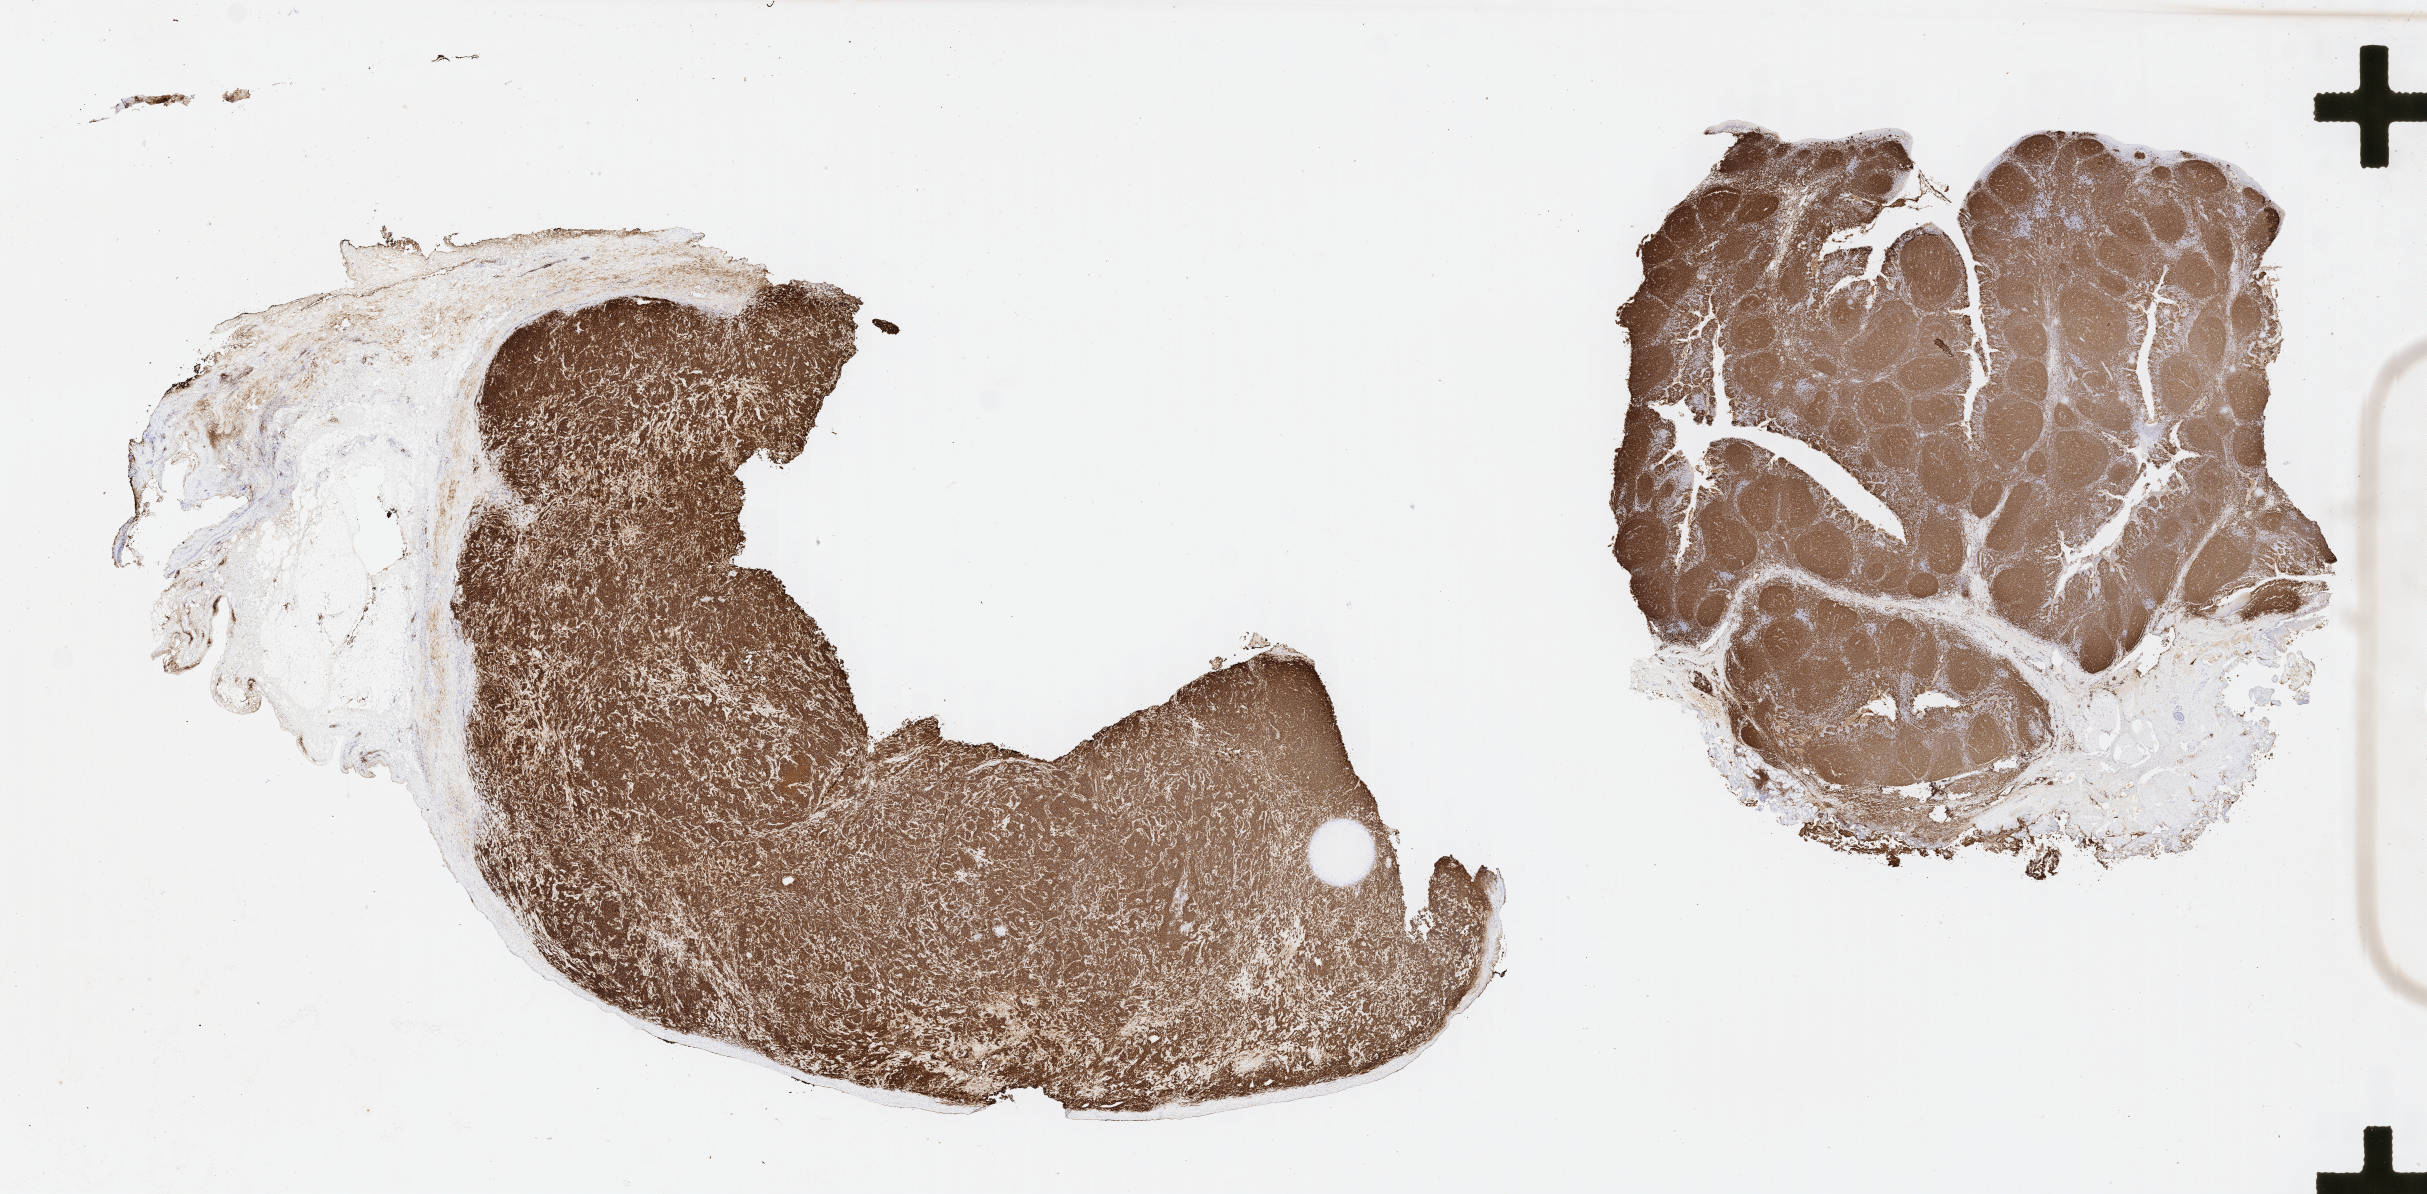
IHC for CD20, whole-slide image, shown as a low-resolution overview of the whole scanned area (about 39.2 x 19.3 mm). Tumor tissue. Anatomic site: bone. Male patient, aged 48.
Histologic diagnosis: Diffuse large B-cell lymphoma, NOS.